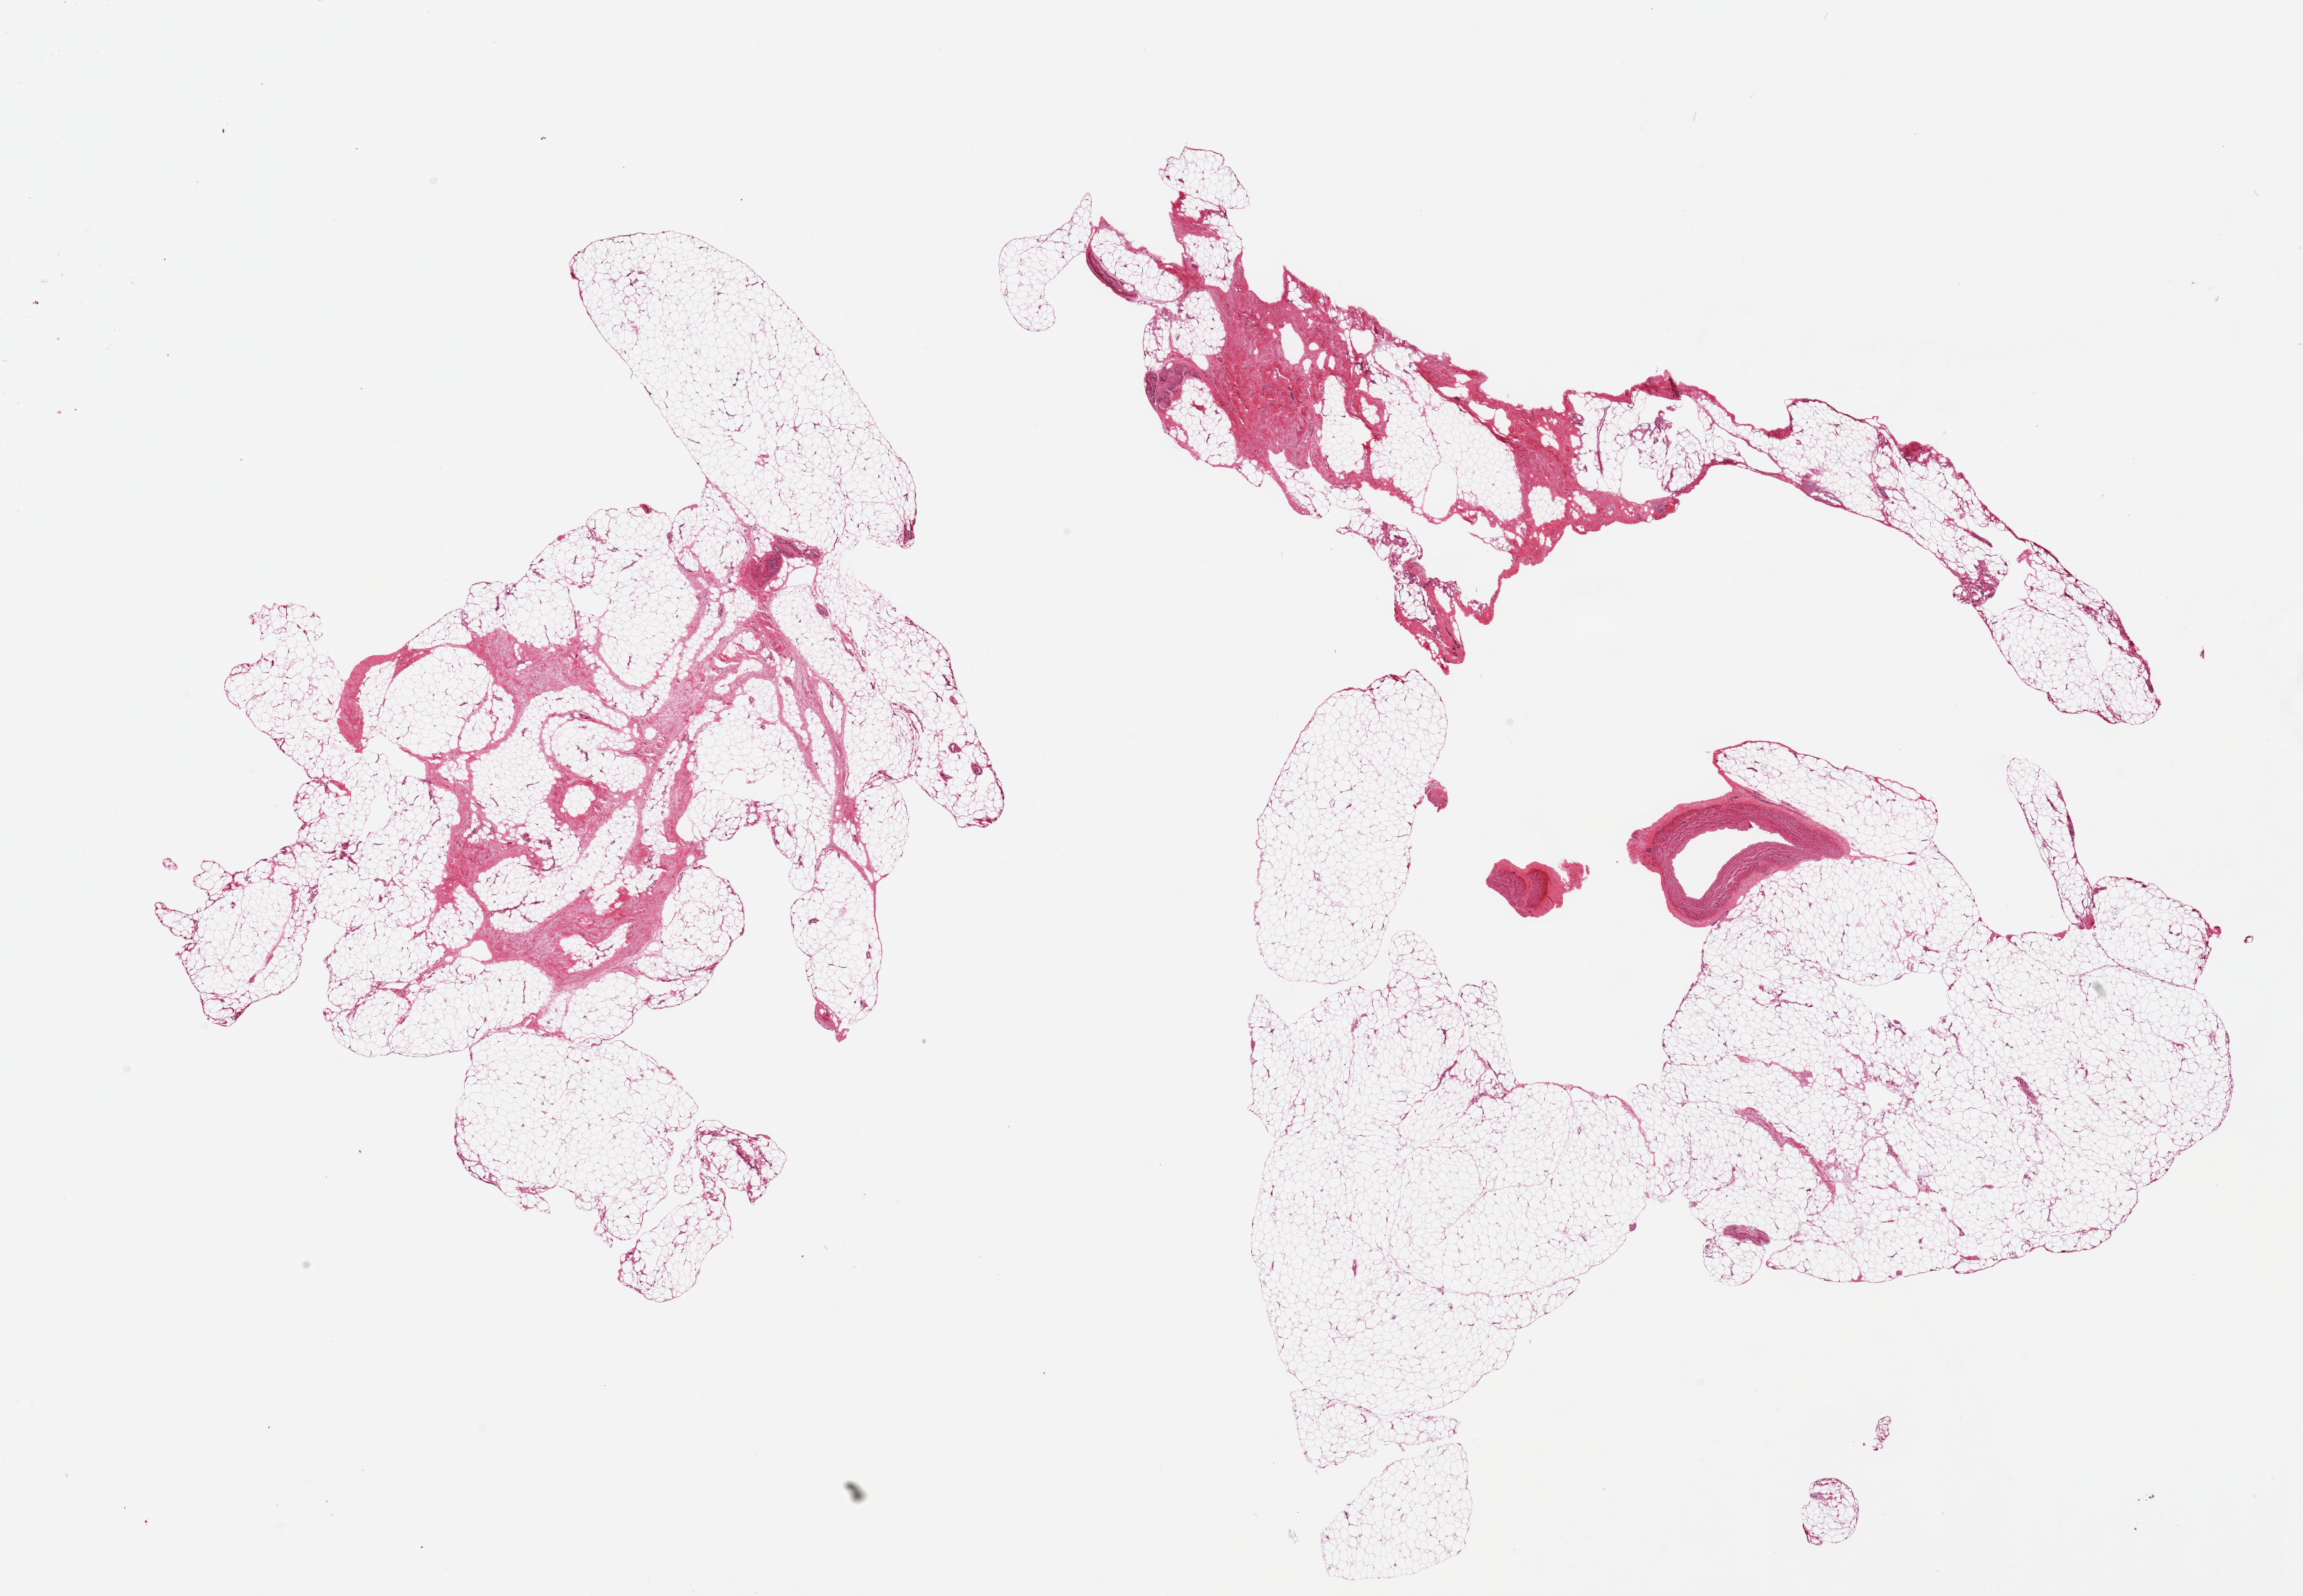
H&E whole-slide image — low-resolution overview of the scanned area, about 25.6 x 17.7 mm, PAXgene-fixed paraffin-embedded (PFPE) section, target tissue: adipose tissue, tissue donor sample. Donor sex: male.
- reviewer comment on this tissue sample: 2 pieces, ~30% fascia/vascular elements